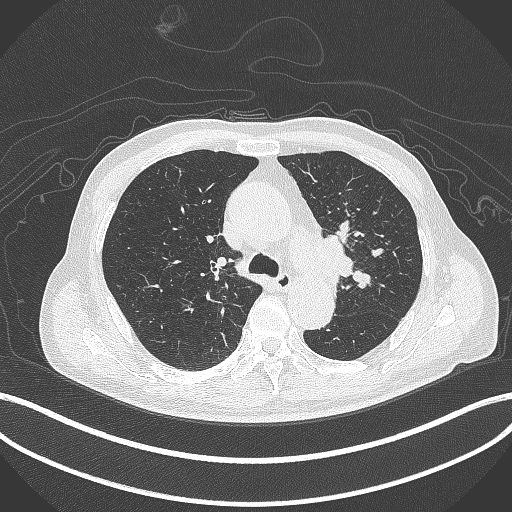
Chest CT, one axial slice. Slice 296 of 417 in the series (ordered by position). Reconstruction kernel B70f. 120 kVp. Lung window (W 1500 / L -600 HU). 1 mm slice thickness. 512 × 512 image matrix. Patient: male, 77 years. Case-level facts recorded for this patient, not image findings: clinical TNM (as recorded): T3 N1 M0.
Structures marked on this image (rectangle marked by the reading radiologist):
- lung tumour (recorded histology: adenocarcinoma): bounding box [x1, y1, x2, y2] px = [321, 230, 366, 284]